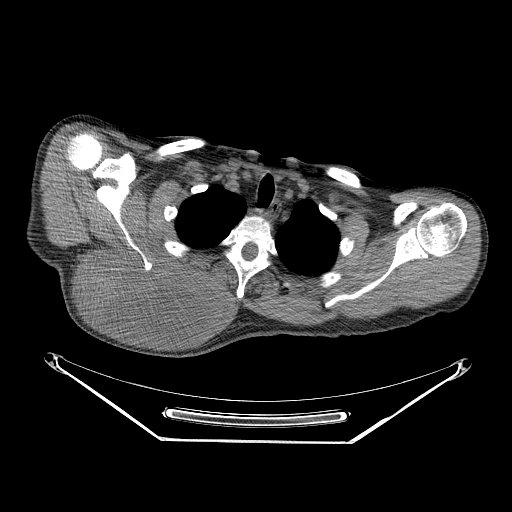
CT of an extremity soft-tissue mass (from a PET/CT study), one axial slice. Reconstruction kernel STANDARD. 140 kVp. Soft-tissue window (W 400 / L 40 HU). 3.75 mm slice thickness. 512 × 512 image matrix, field of view 500 × 500 mm. Male patient. Case-level facts recorded for this patient, not image findings: histological type: pleiomorphic spindle cell undifferentiated; grade: high; site of the primary tumour: right parascapusular.
Outlined on this slice (expert contour drawn on MRI and transferred to this co-registered scan by the dataset authors):
- gross tumour volume including surrounding oedema: bounding box <78,247,234,334> (left, top, right, bottom; pixels)
- gross tumour volume (mass): <78,251,220,332>